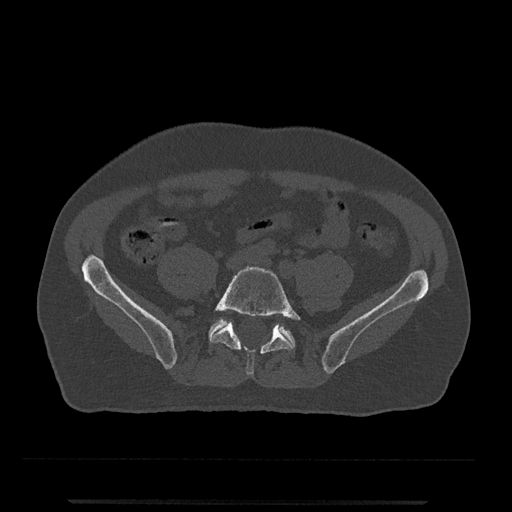
CT including the spine, one axial slice. Slice 65 of 797 in the series (ordered by position). Reconstruction kernel Br40s/3. 120 kVp. Bone window (W 1800 / L 400 HU). 0.5 mm slice thickness. 512 × 512 image matrix, field of view 419 × 419 mm. Patient: male, 63 years. From the clinical record (not read from this slice): primary cancer: prostate.
Annotated regions visible in this slice (semi-automatic segmentation, software-assisted and operator-edited):
- L5 vertebra: bounding box [x1, y1, x2, y2] px = [211, 266, 301, 376]